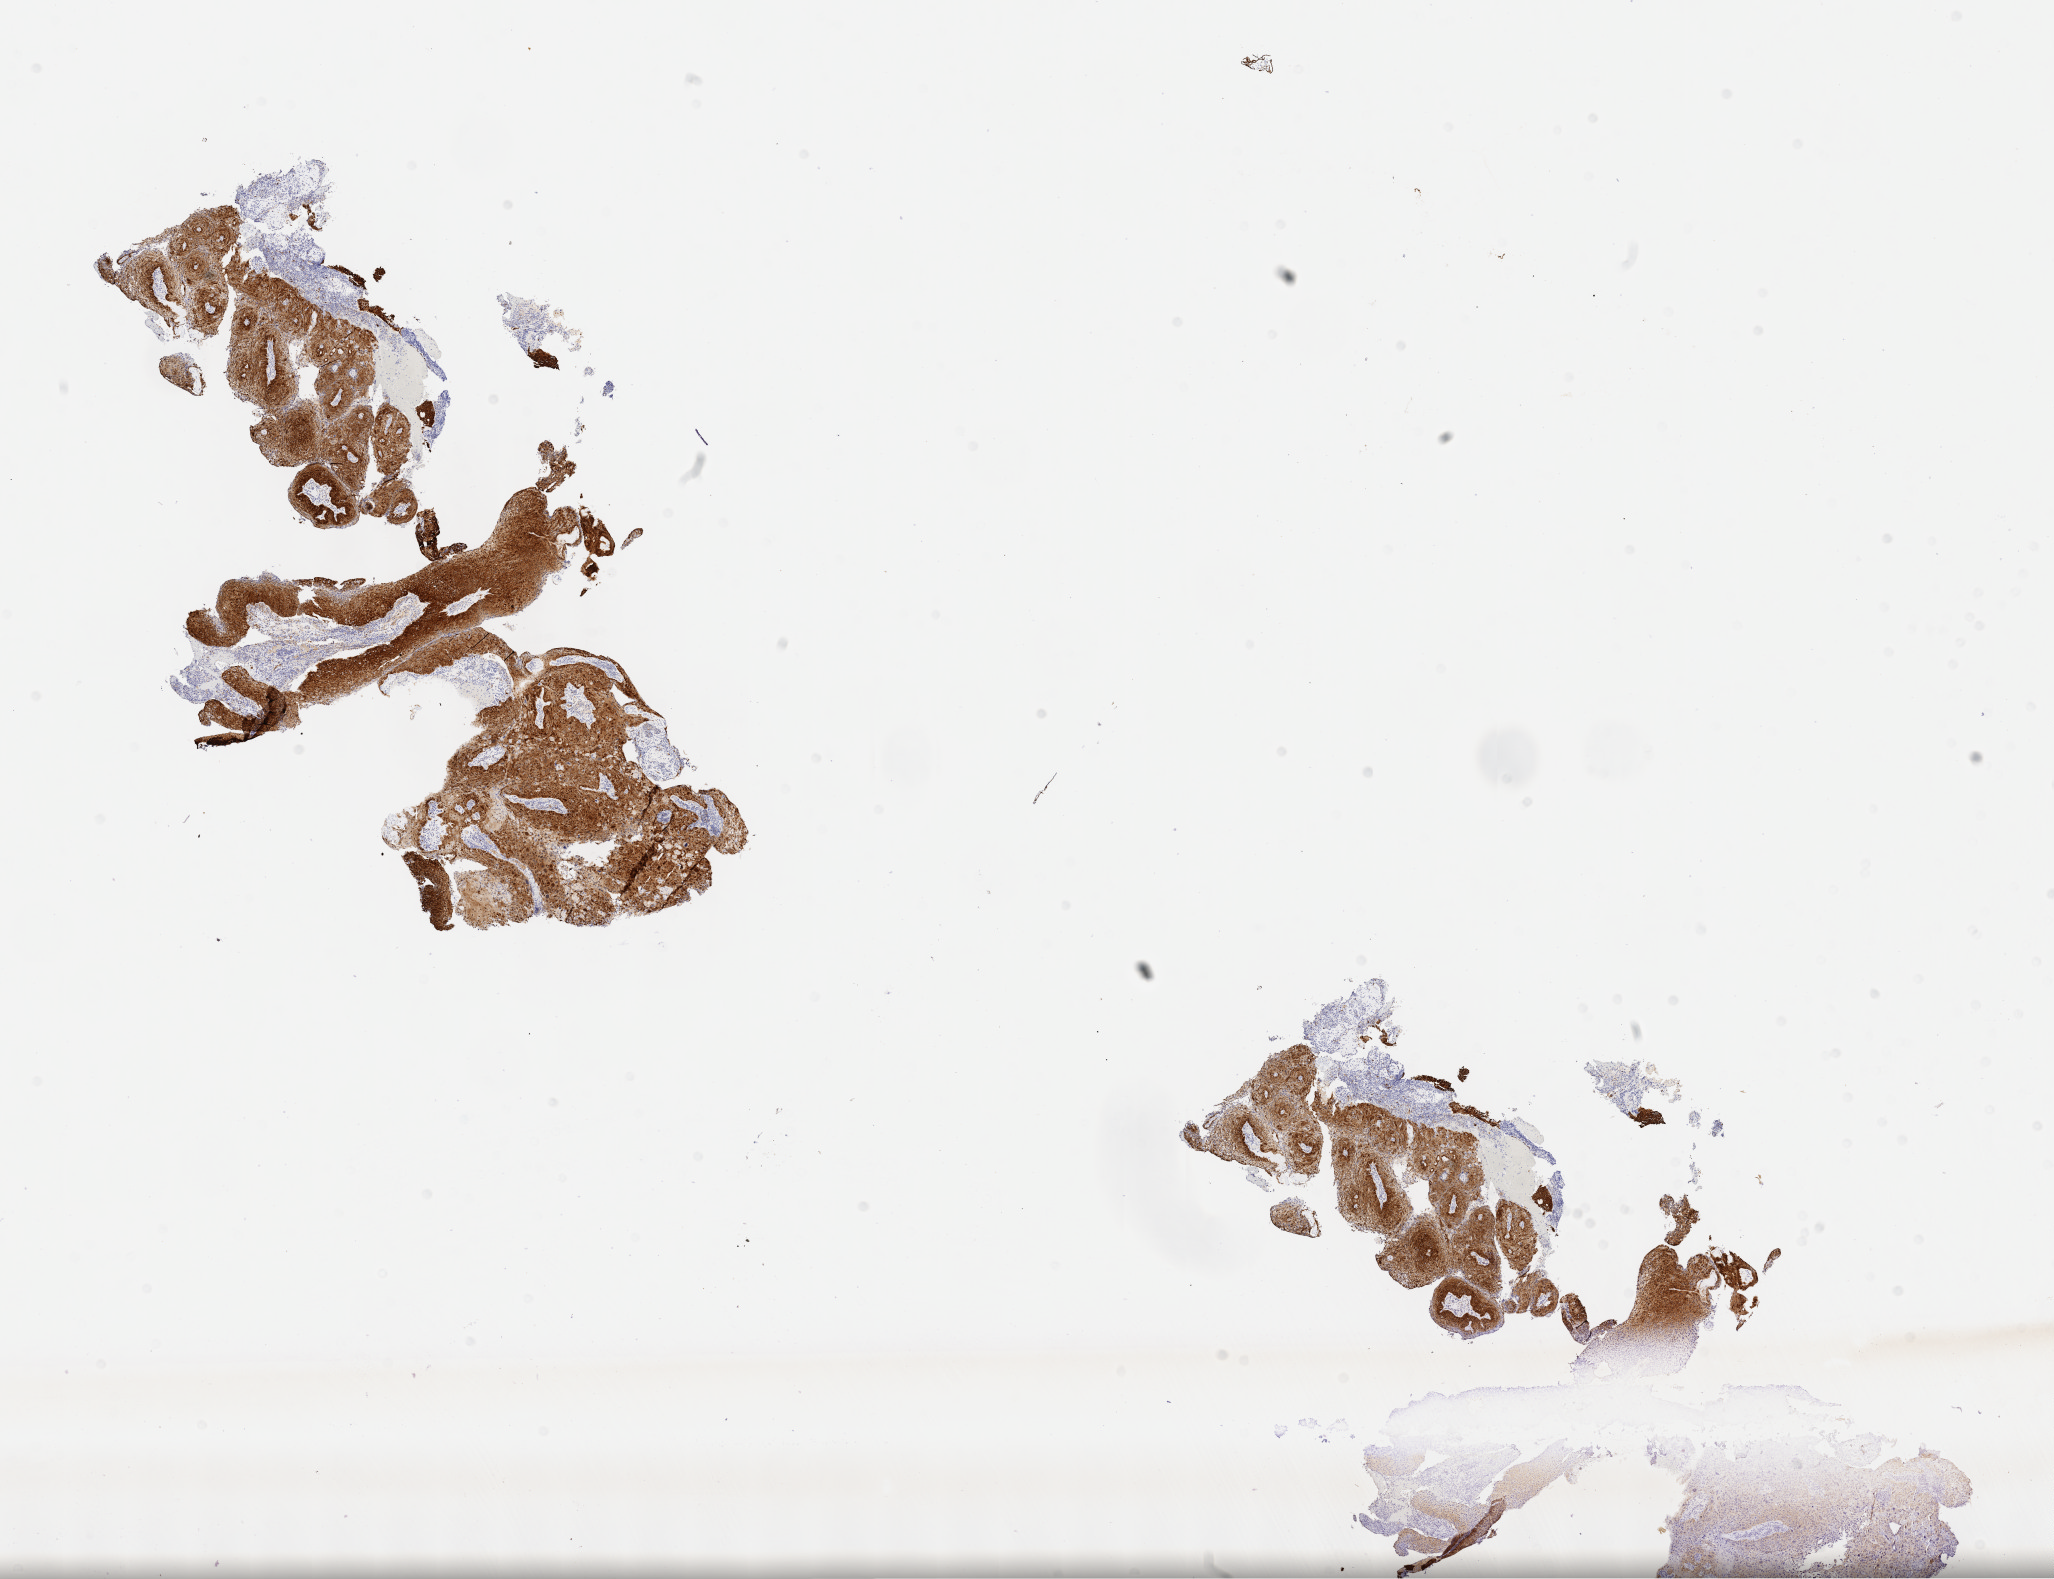
IHC for p16 (p16INK4a), whole-slide image, shown as a low-resolution overview of the whole scanned area (about 16.6 x 12.8 mm); tumor tissue; anatomic site: cervix. Female patient, 44 years old.
Diagnosis: Squamous cell carcinoma, keratinizing, NOS.